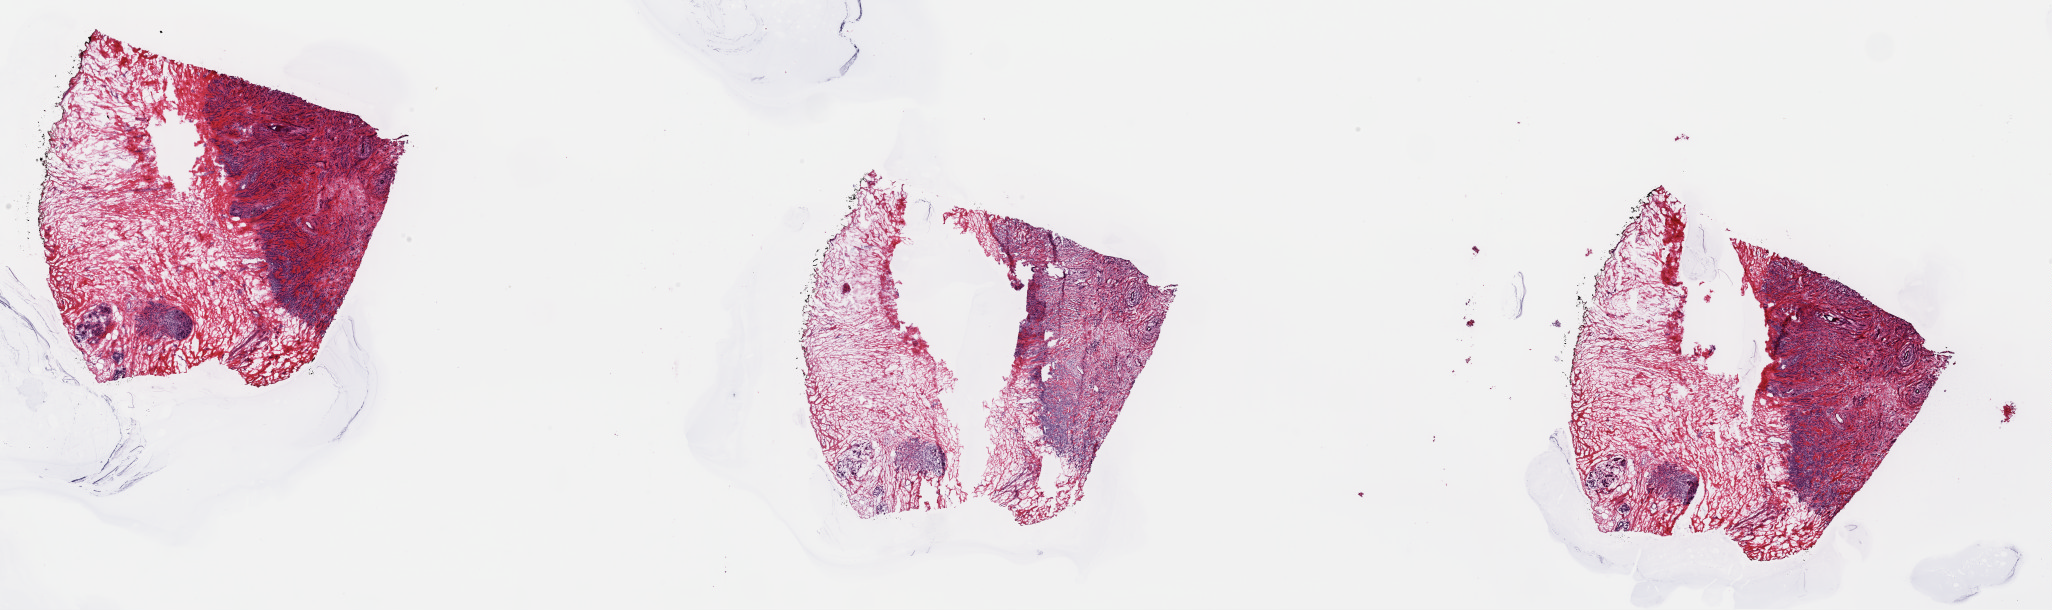
H&E whole-slide image — shown as a low-resolution overview of the whole scanned area (about 32.4 x 9.6 mm, from a 40x scan). Frozen section. Breast, primary tumour sample. Female, age 45 years at initial diagnosis. Composition of this section per pathologist review: tumour cells 25%, tumour nuclei 70%.
Histologic diagnosis: Lobular carcinoma, NOS.